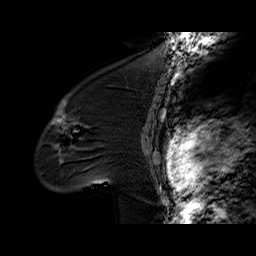
Breast MRI (dynamic contrast-enhanced), one sagittal slice; slice 45 of 60 in the series (ordered by position); dynamic contrast-enhanced series, time point 2 of 6 at this slice position (early post-contrast); 1.5 T; TE 6.2 ms, TR 32.4 ms; 256 × 256 image matrix, field of view 200 × 200 mm. Female patient. Case-level facts recorded for this patient, not image findings: setting: breast cancer imaged before/during neoadjuvant chemotherapy; receptor status: triple-negative.
Annotated regions visible in this slice (semi-automatic segmentation, software-assisted and operator-edited):
- analysis volume of interest (the breast-tissue region the enhancement analysis was run in; not a lesion): bounding box (x1, y1, x2, y2) in pixels: (36, 97, 134, 192)
- tumour enhancement mask (voxels above the 100 % enhancement threshold inside the analysis volume of interest): (53, 101, 74, 124)